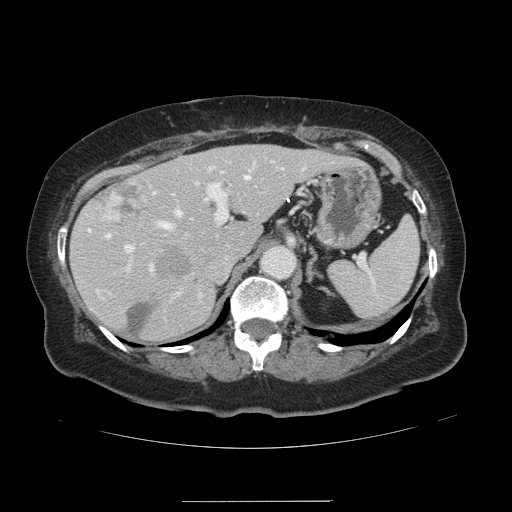
Contrast-enhanced abdominal CT, one axial slice. Position 87 of 141 along the scan axis. Soft-tissue window (W 400 / L 40 HU). 2.5 mm slice thickness. 512 × 512 image matrix, field of view 393 × 393 mm. Female patient, age 74 years. From the clinical record (not read from this slice): diagnosis: colorectal cancer liver metastases, imaged before liver resection; multiple liver metastases: yes; largest metastasis: 7 cm; chemotherapy before resection: no.
Outlined on this slice (manually delineated by an expert):
- hepatic veins: bounding box <106,175,249,298> (left, top, right, bottom; pixels)
- liver: <72,145,343,340>
- planned liver remnant (the part of the liver to remain after resection): <72,145,343,339>
- portal vein (with intrahepatic branches): <125,167,304,271>
- liver metastasis: <96,179,156,234>
- liver metastasis: <128,303,152,333>
- liver metastasis: <162,246,192,276>